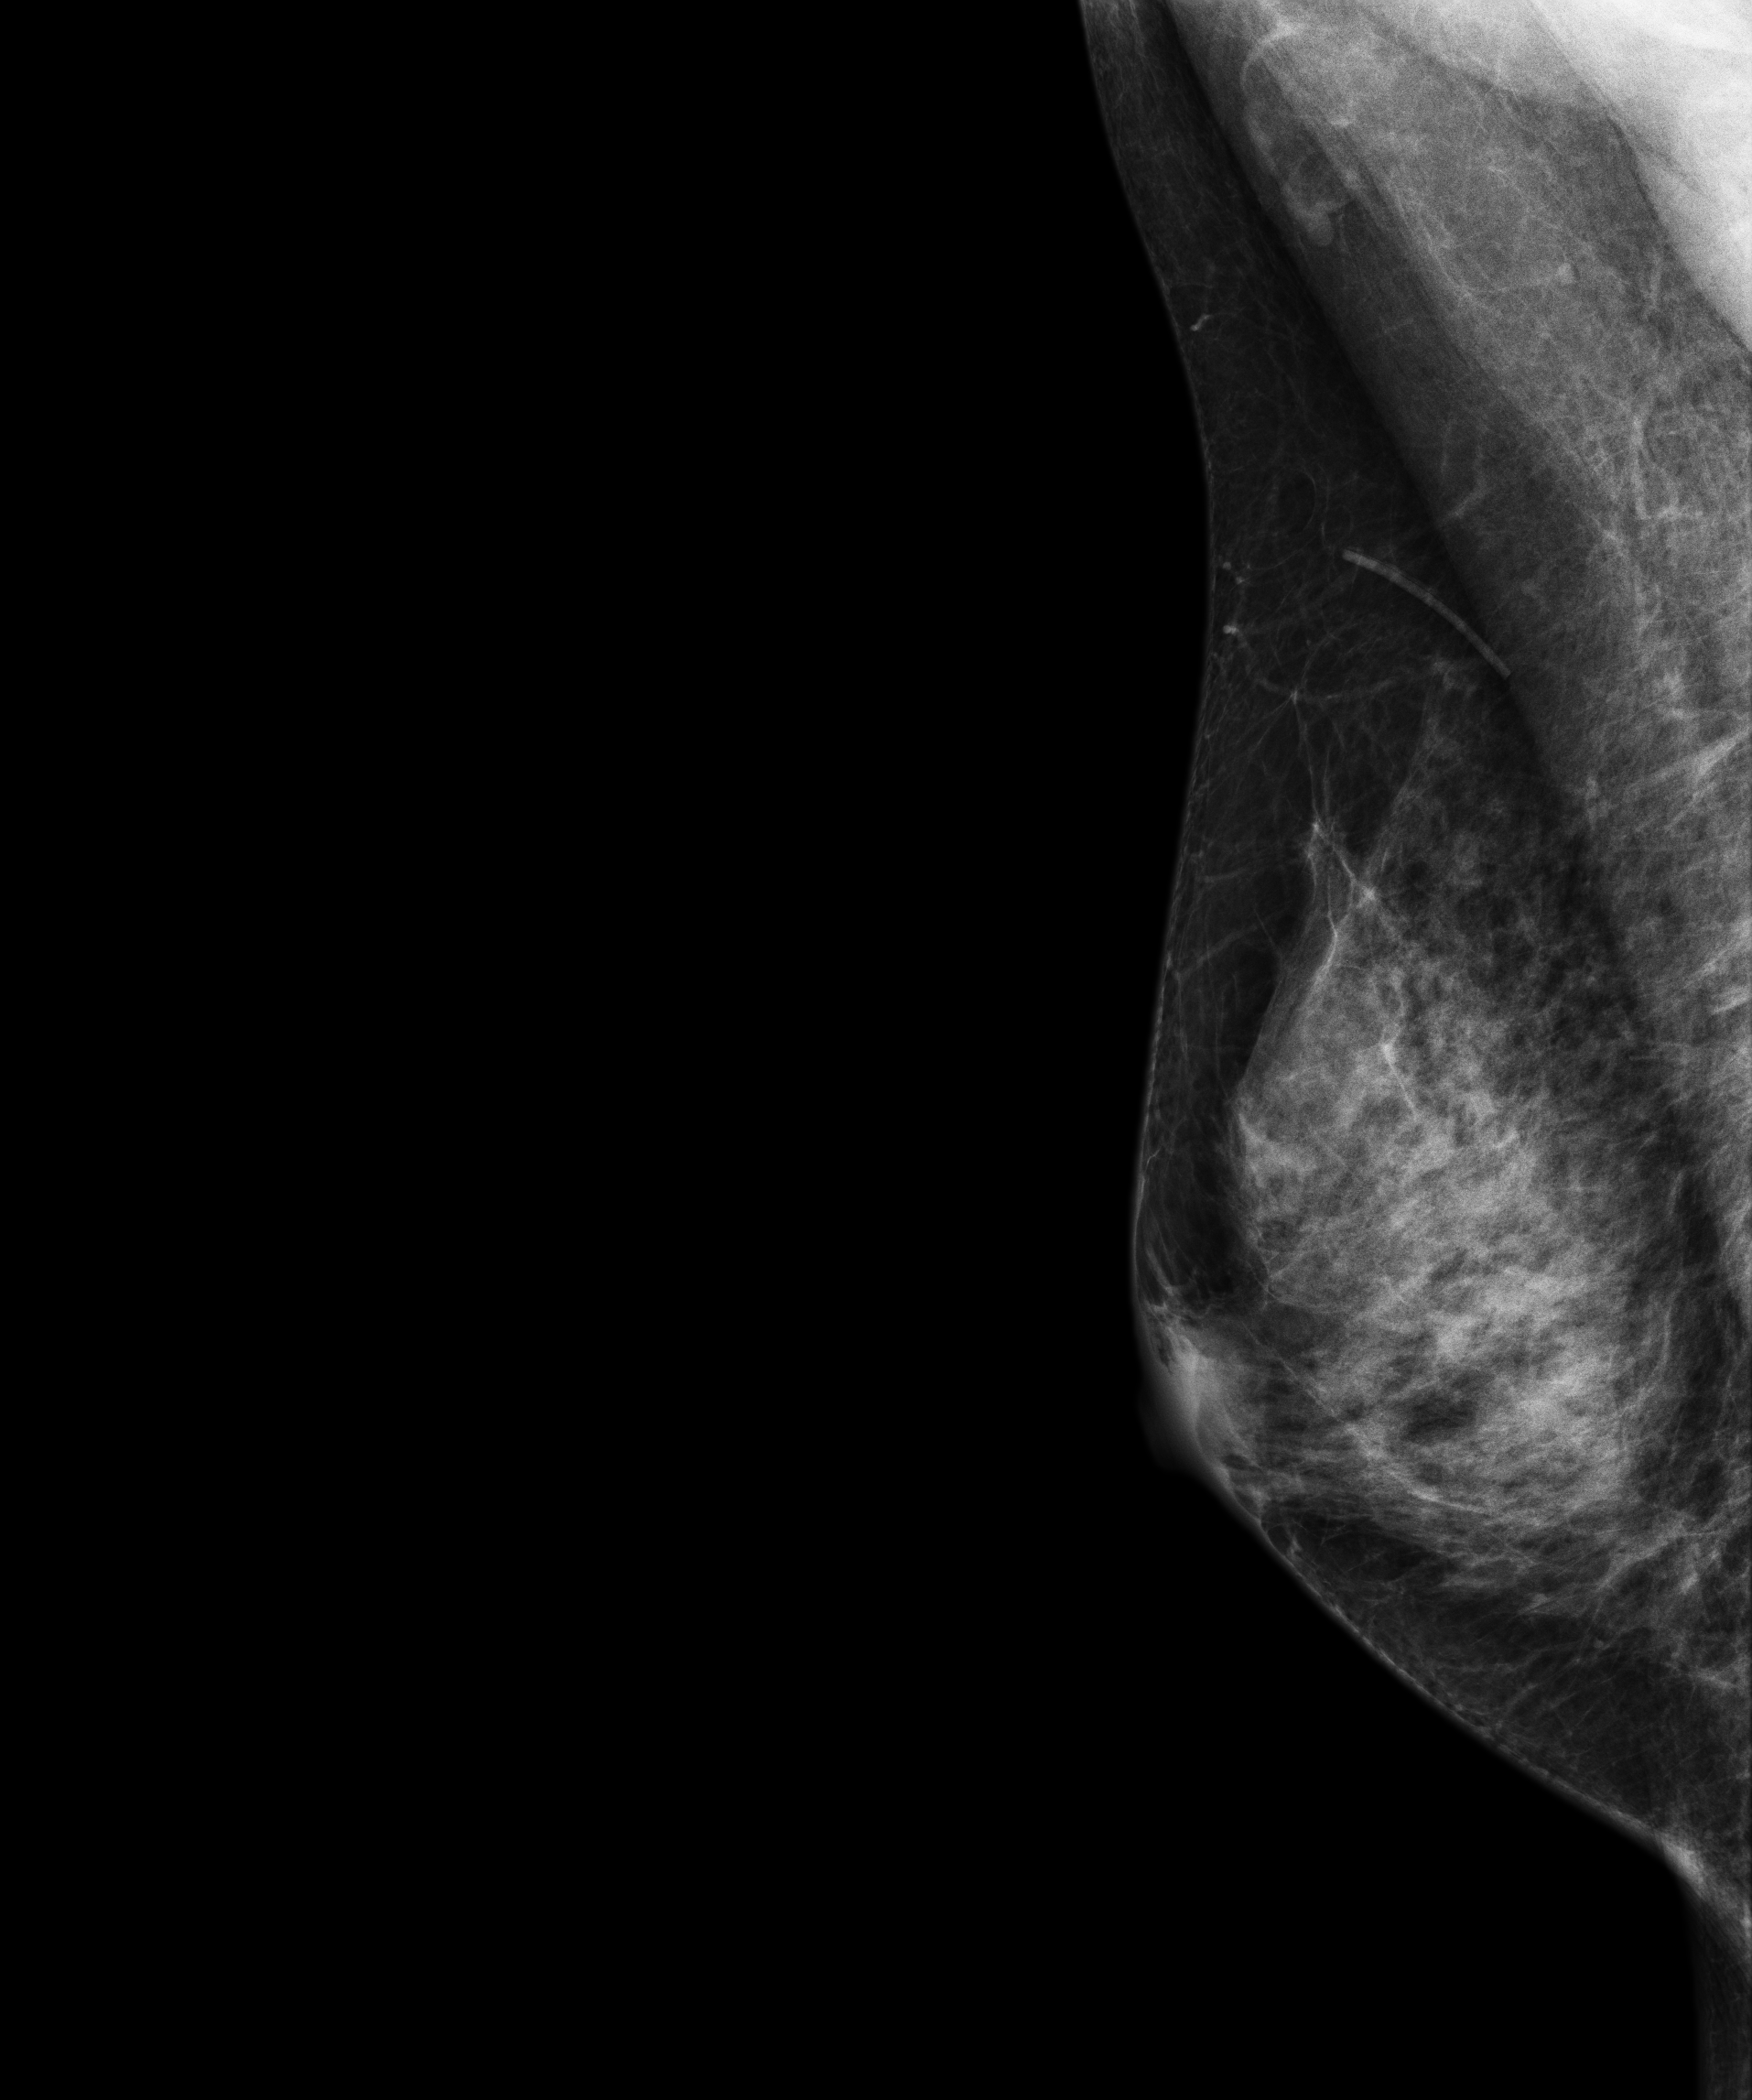
Full-field digital mammogram (FFDM), right breast, medio-lateral oblique projection, screening examination, compressed breast thickness 56 mm. Patient: female, 55 years.
- breast density at the screening exam (both breasts): extremely dense (BI-RADS density category d)
- final BI-RADS category for the screening round (tomosynthesis exam, both breasts): category 1
- recall: no recall after this screen